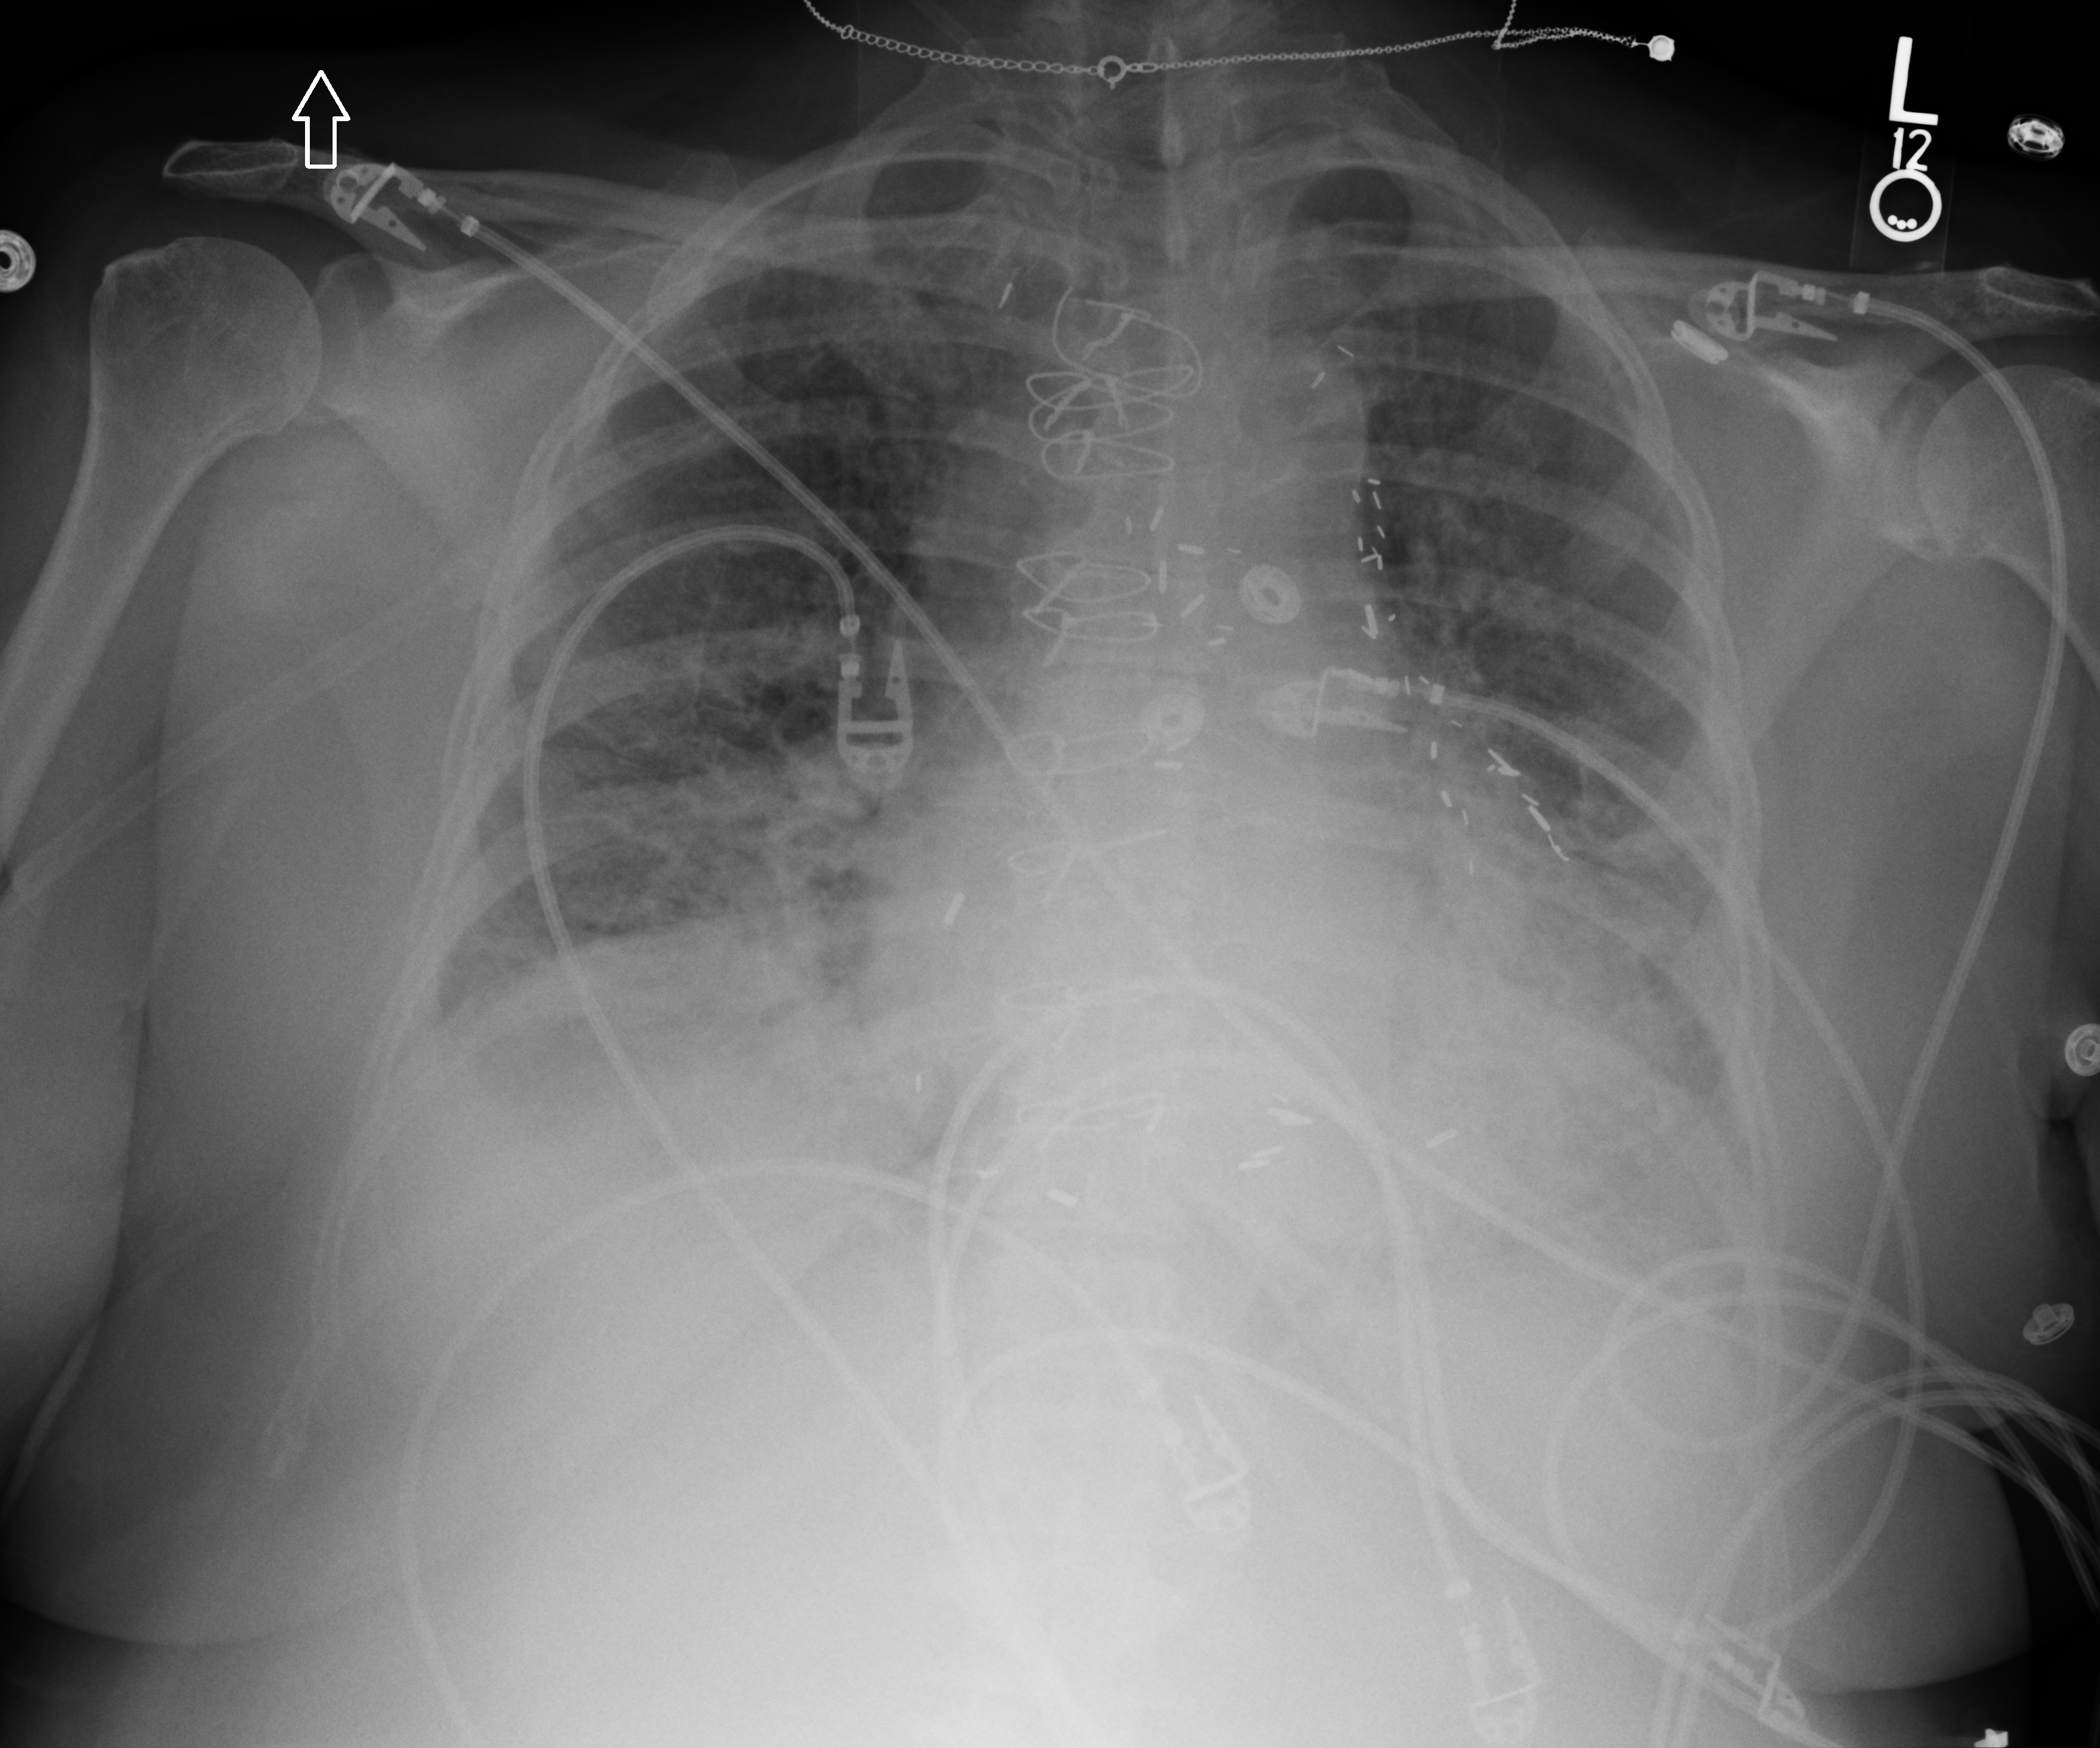
Bedside chest radiograph (computed radiography); anteroposterior (AP) projection. Female patient hospitalised with COVID-19, age 60–74 years.
Admission-level facts for this patient (not findings on this image; timing relative to this image not recorded):
- COPD (admission record): no
- admitted to intensive care during this hospital stay: yes